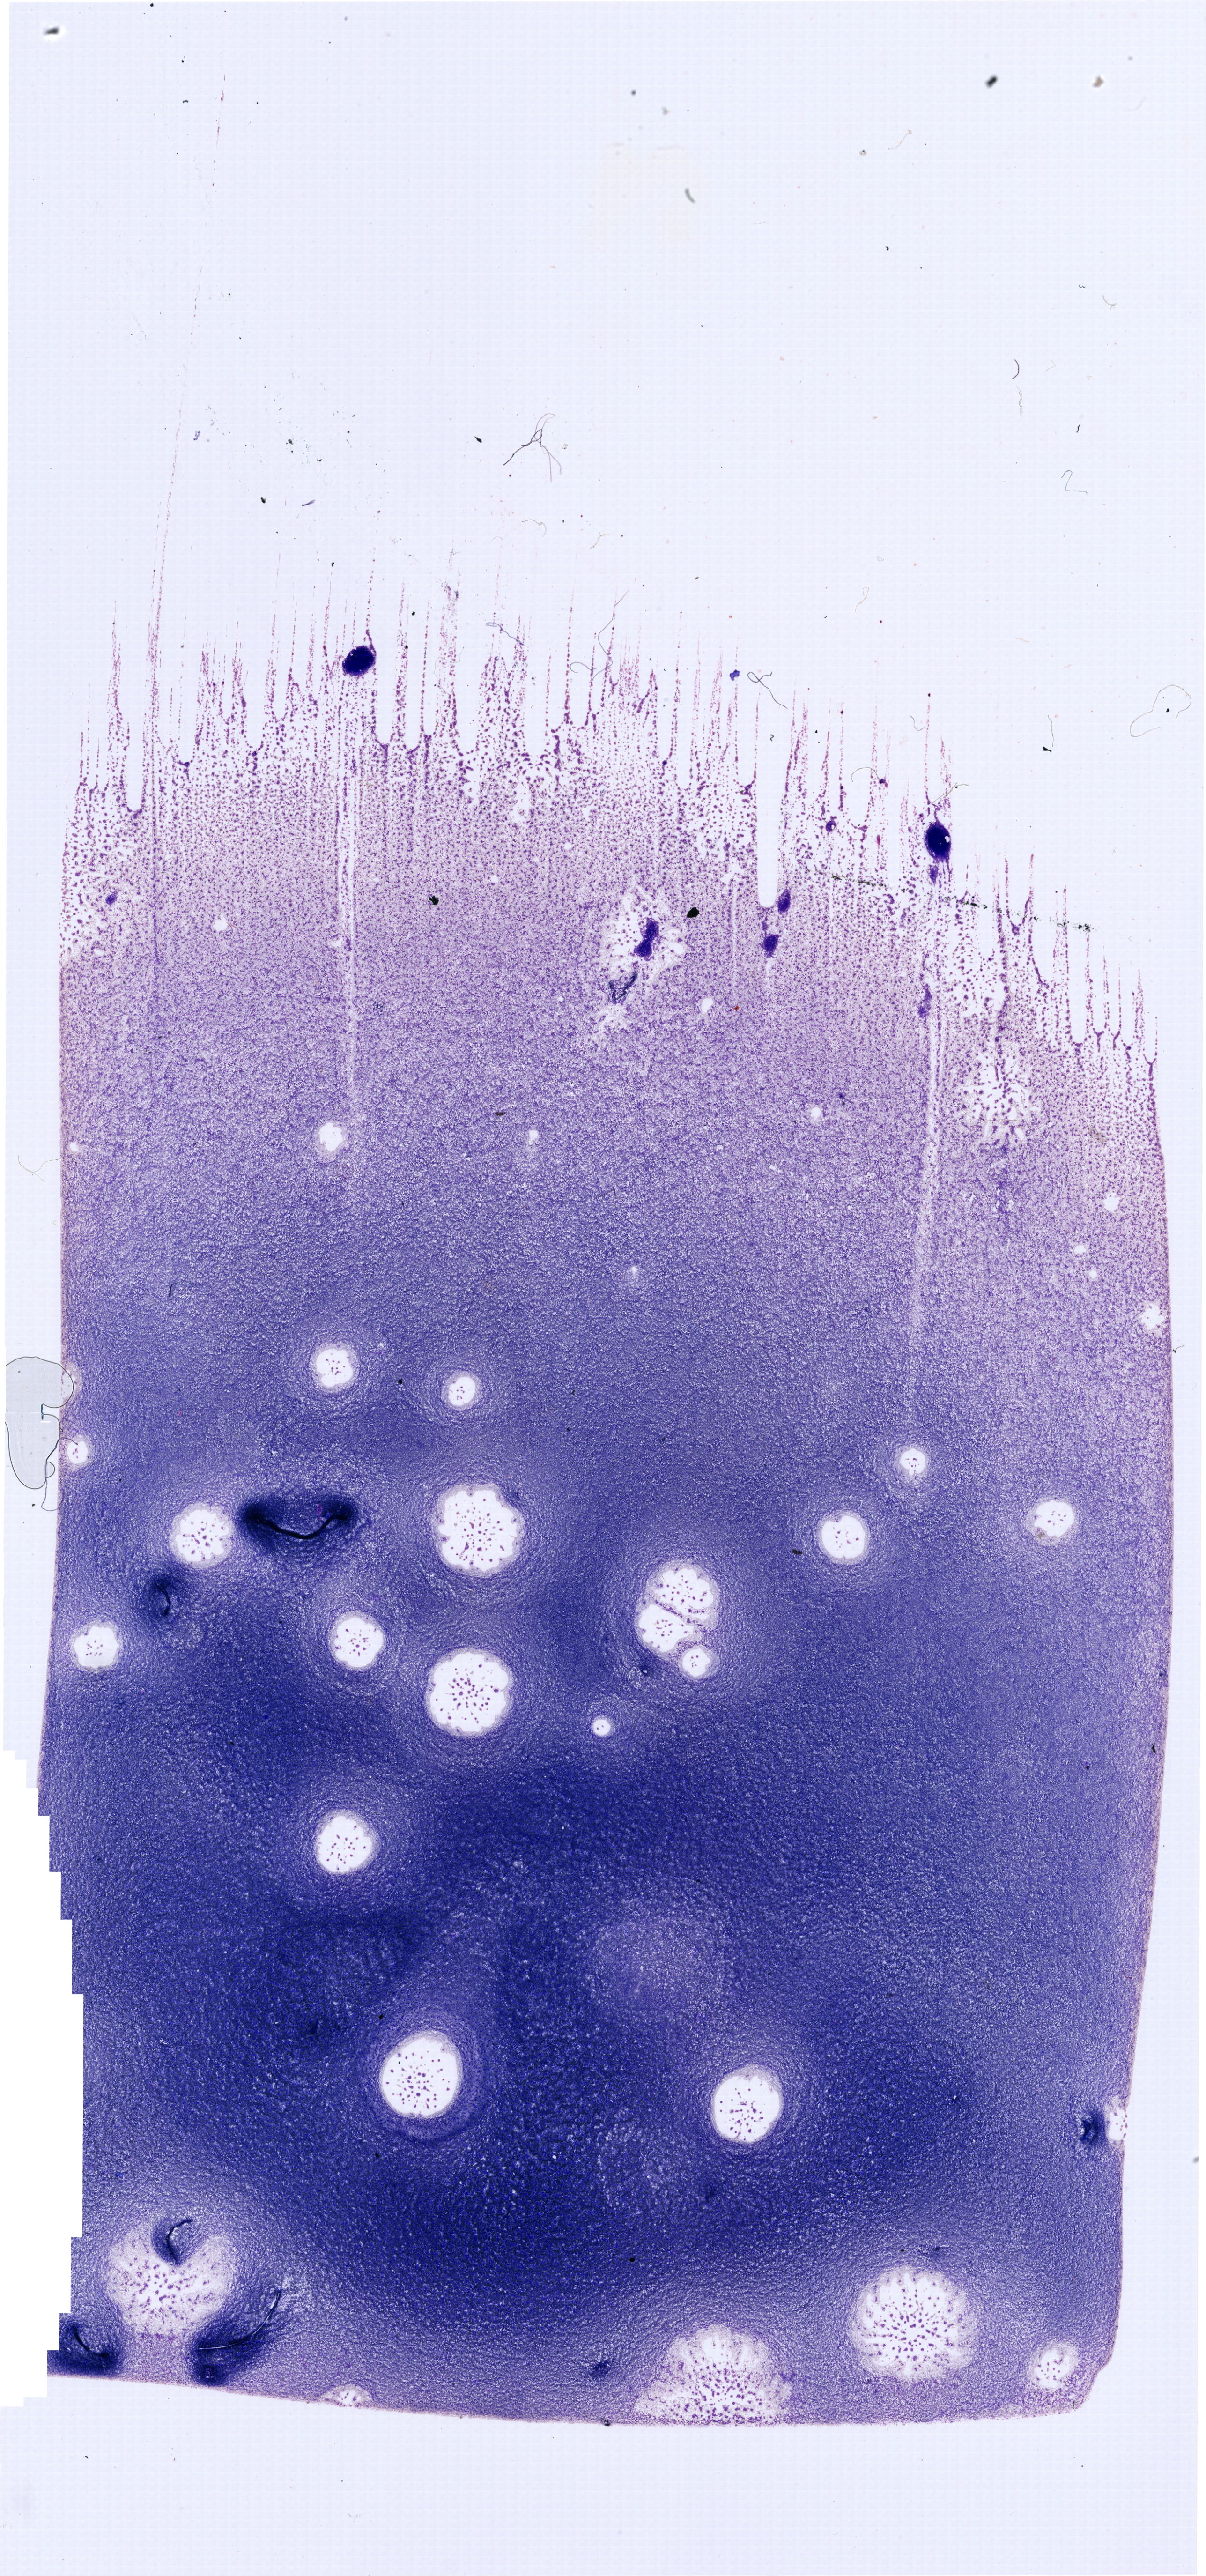
May-Grünwald-Giemsa (MGG)-stained marrow aspirate smear (whole slide) — whole scanned area (about 20.1 x 42.9 mm) shown as a low-resolution overview. Female patient.
* diagnosis: T Acute Lymphoblastic Leukemia